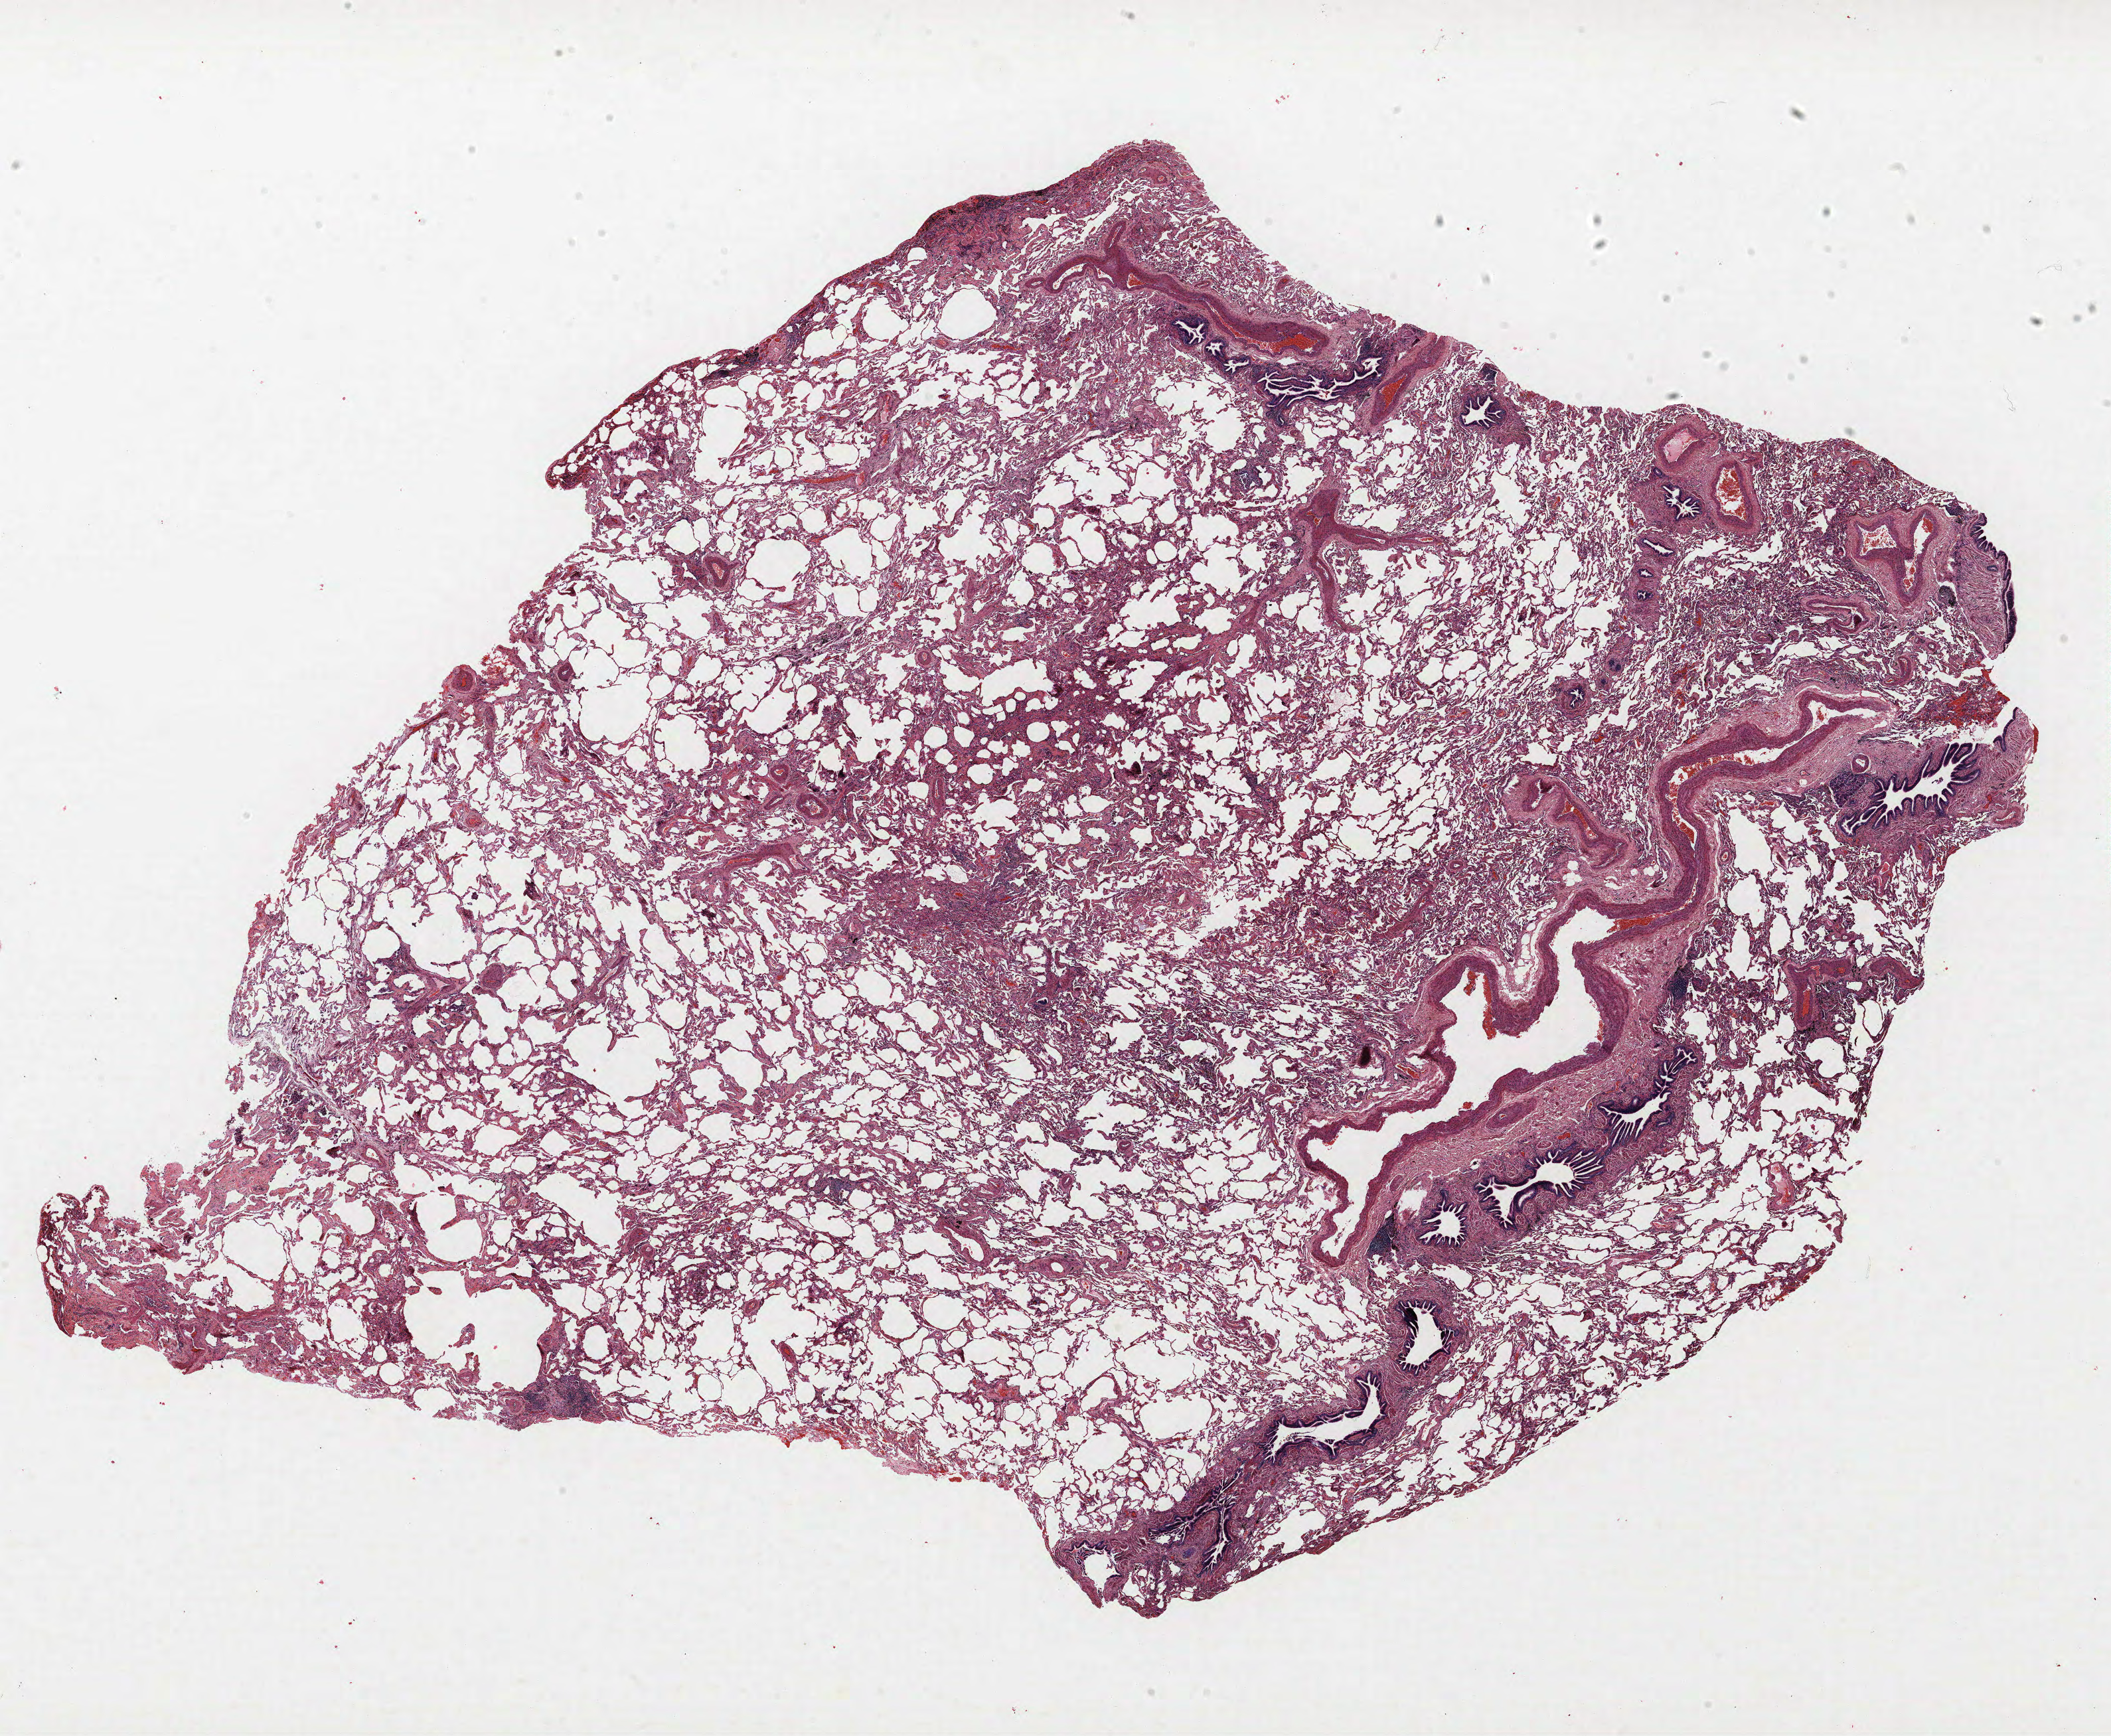
H&E whole-slide image, whole scanned area (about 25.4 x 20.9 mm, acquisition: 40x scan) shown as a low-resolution overview, formalin-fixed paraffin-embedded (FFPE) section, lung tissue. Male, age 67 at enrolment. Current smoker at enrolment. Grade: well differentiated (G1).
Participant's lung-cancer diagnosis: Bronchiolo-alveolar carcinoma, non-mucinous. Tumour size (pathology): 65 mm. Stage (AJCC 6th edition): IB. Primary tumour location (clinical record): right lower lobe.